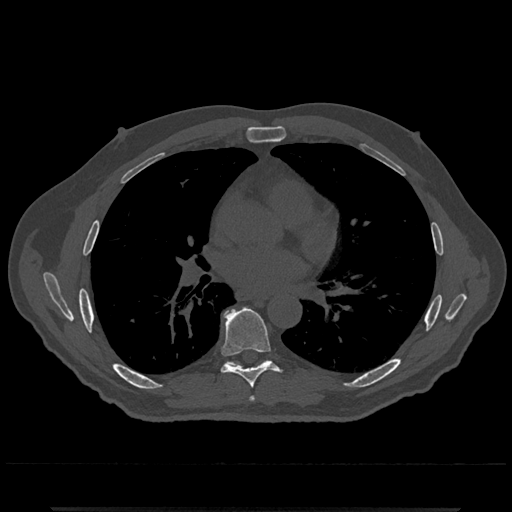
CT including the spine, one axial slice; slice 715 of 797 in the series (ordered by position); 120 kVp; bone window (W 1800 / L 400 HU); 0.5 mm slice thickness; 512 × 512 image matrix, field of view 393 × 393 mm. Male patient, age 67 years. Case-level facts recorded for this patient, not image findings: primary cancer: prostate.
Outlined on this slice (semi-automatic segmentation, software-assisted and operator-edited):
- T6 vertebra: bounding box (x1, y1, x2, y2) in pixels: (249, 396, 255, 401)
- T7 vertebra: (220, 308, 279, 388)
- T8 vertebra: (225, 359, 269, 366)